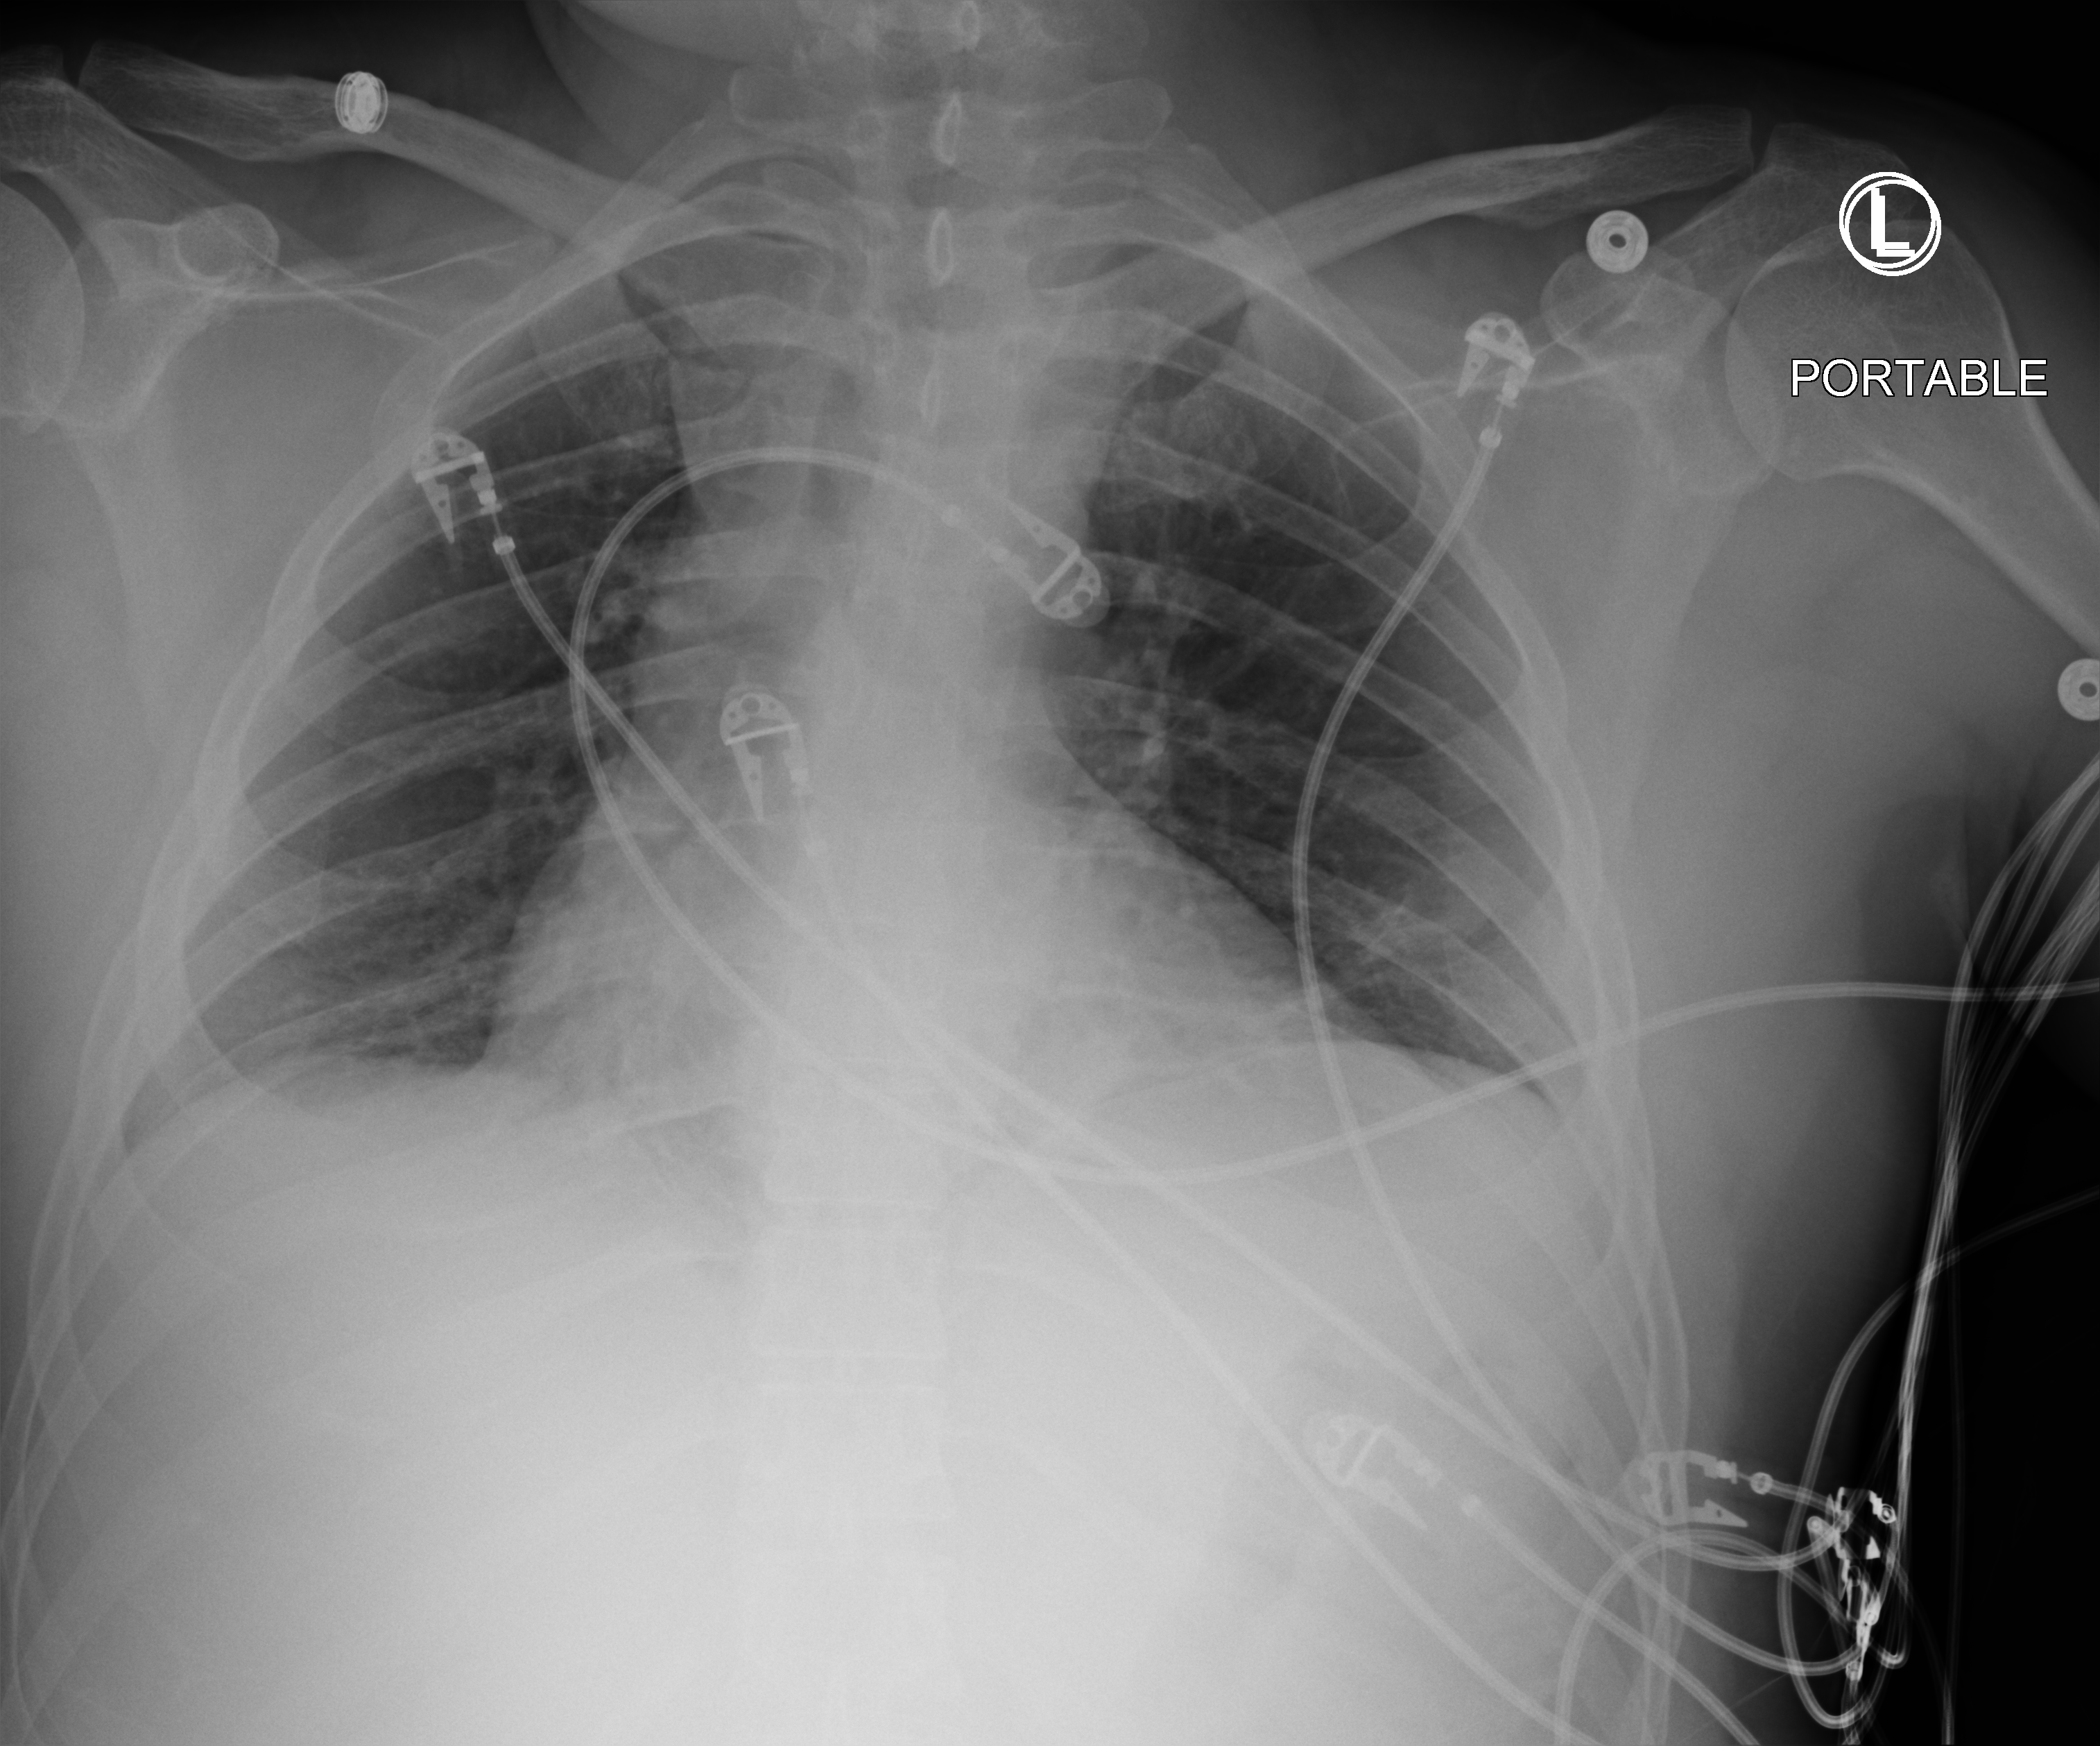
Portable chest radiograph, anteroposterior (AP) projection. Male patient hospitalised with COVID-19, age 18–59 years.
Hospital-stay facts (about this admission, not read from this image; timing relative to this image not recorded):
- mechanically ventilated during this hospital stay: yes
- other chronic lung disease (admission record): no